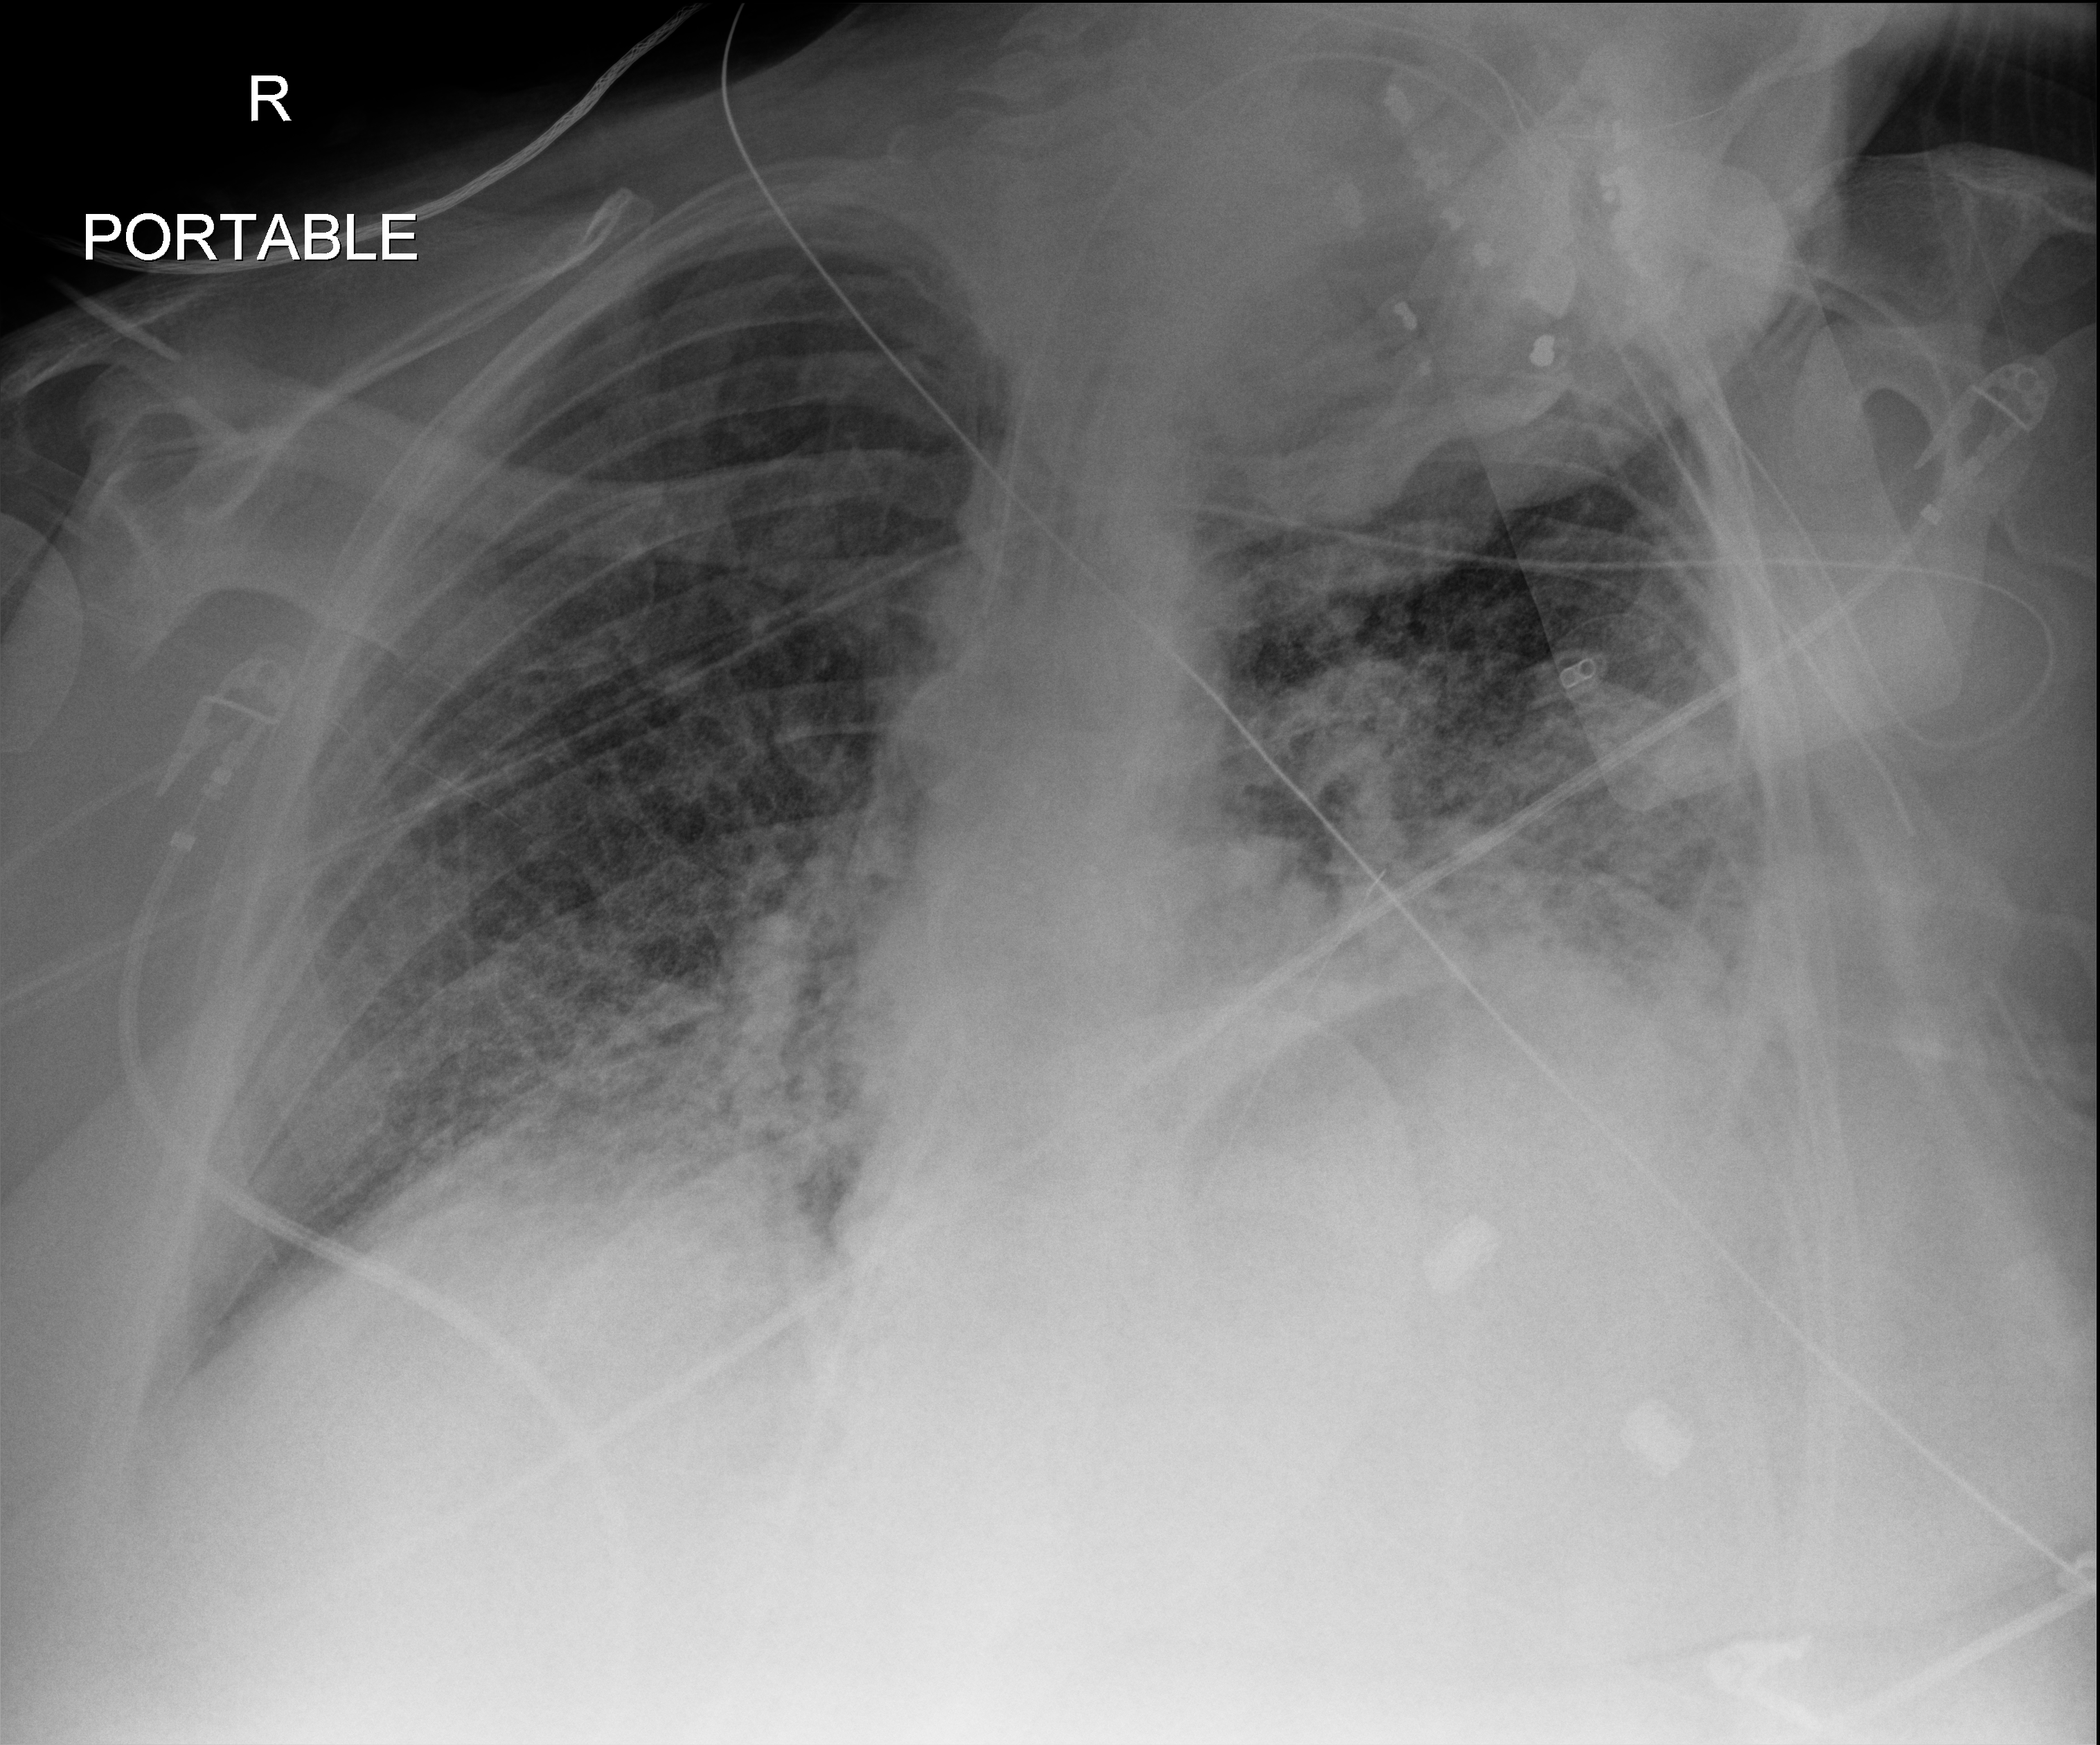
Bedside chest radiograph (digital radiography). Patient hospitalised with COVID-19, aged 18–59 years.
From the hospital-stay record, not from the radiograph (when in the stay this image was taken is not recorded): admitted to intensive care during this hospital stay: yes; mechanically ventilated during this hospital stay: yes; length of hospital stay: 28 days.